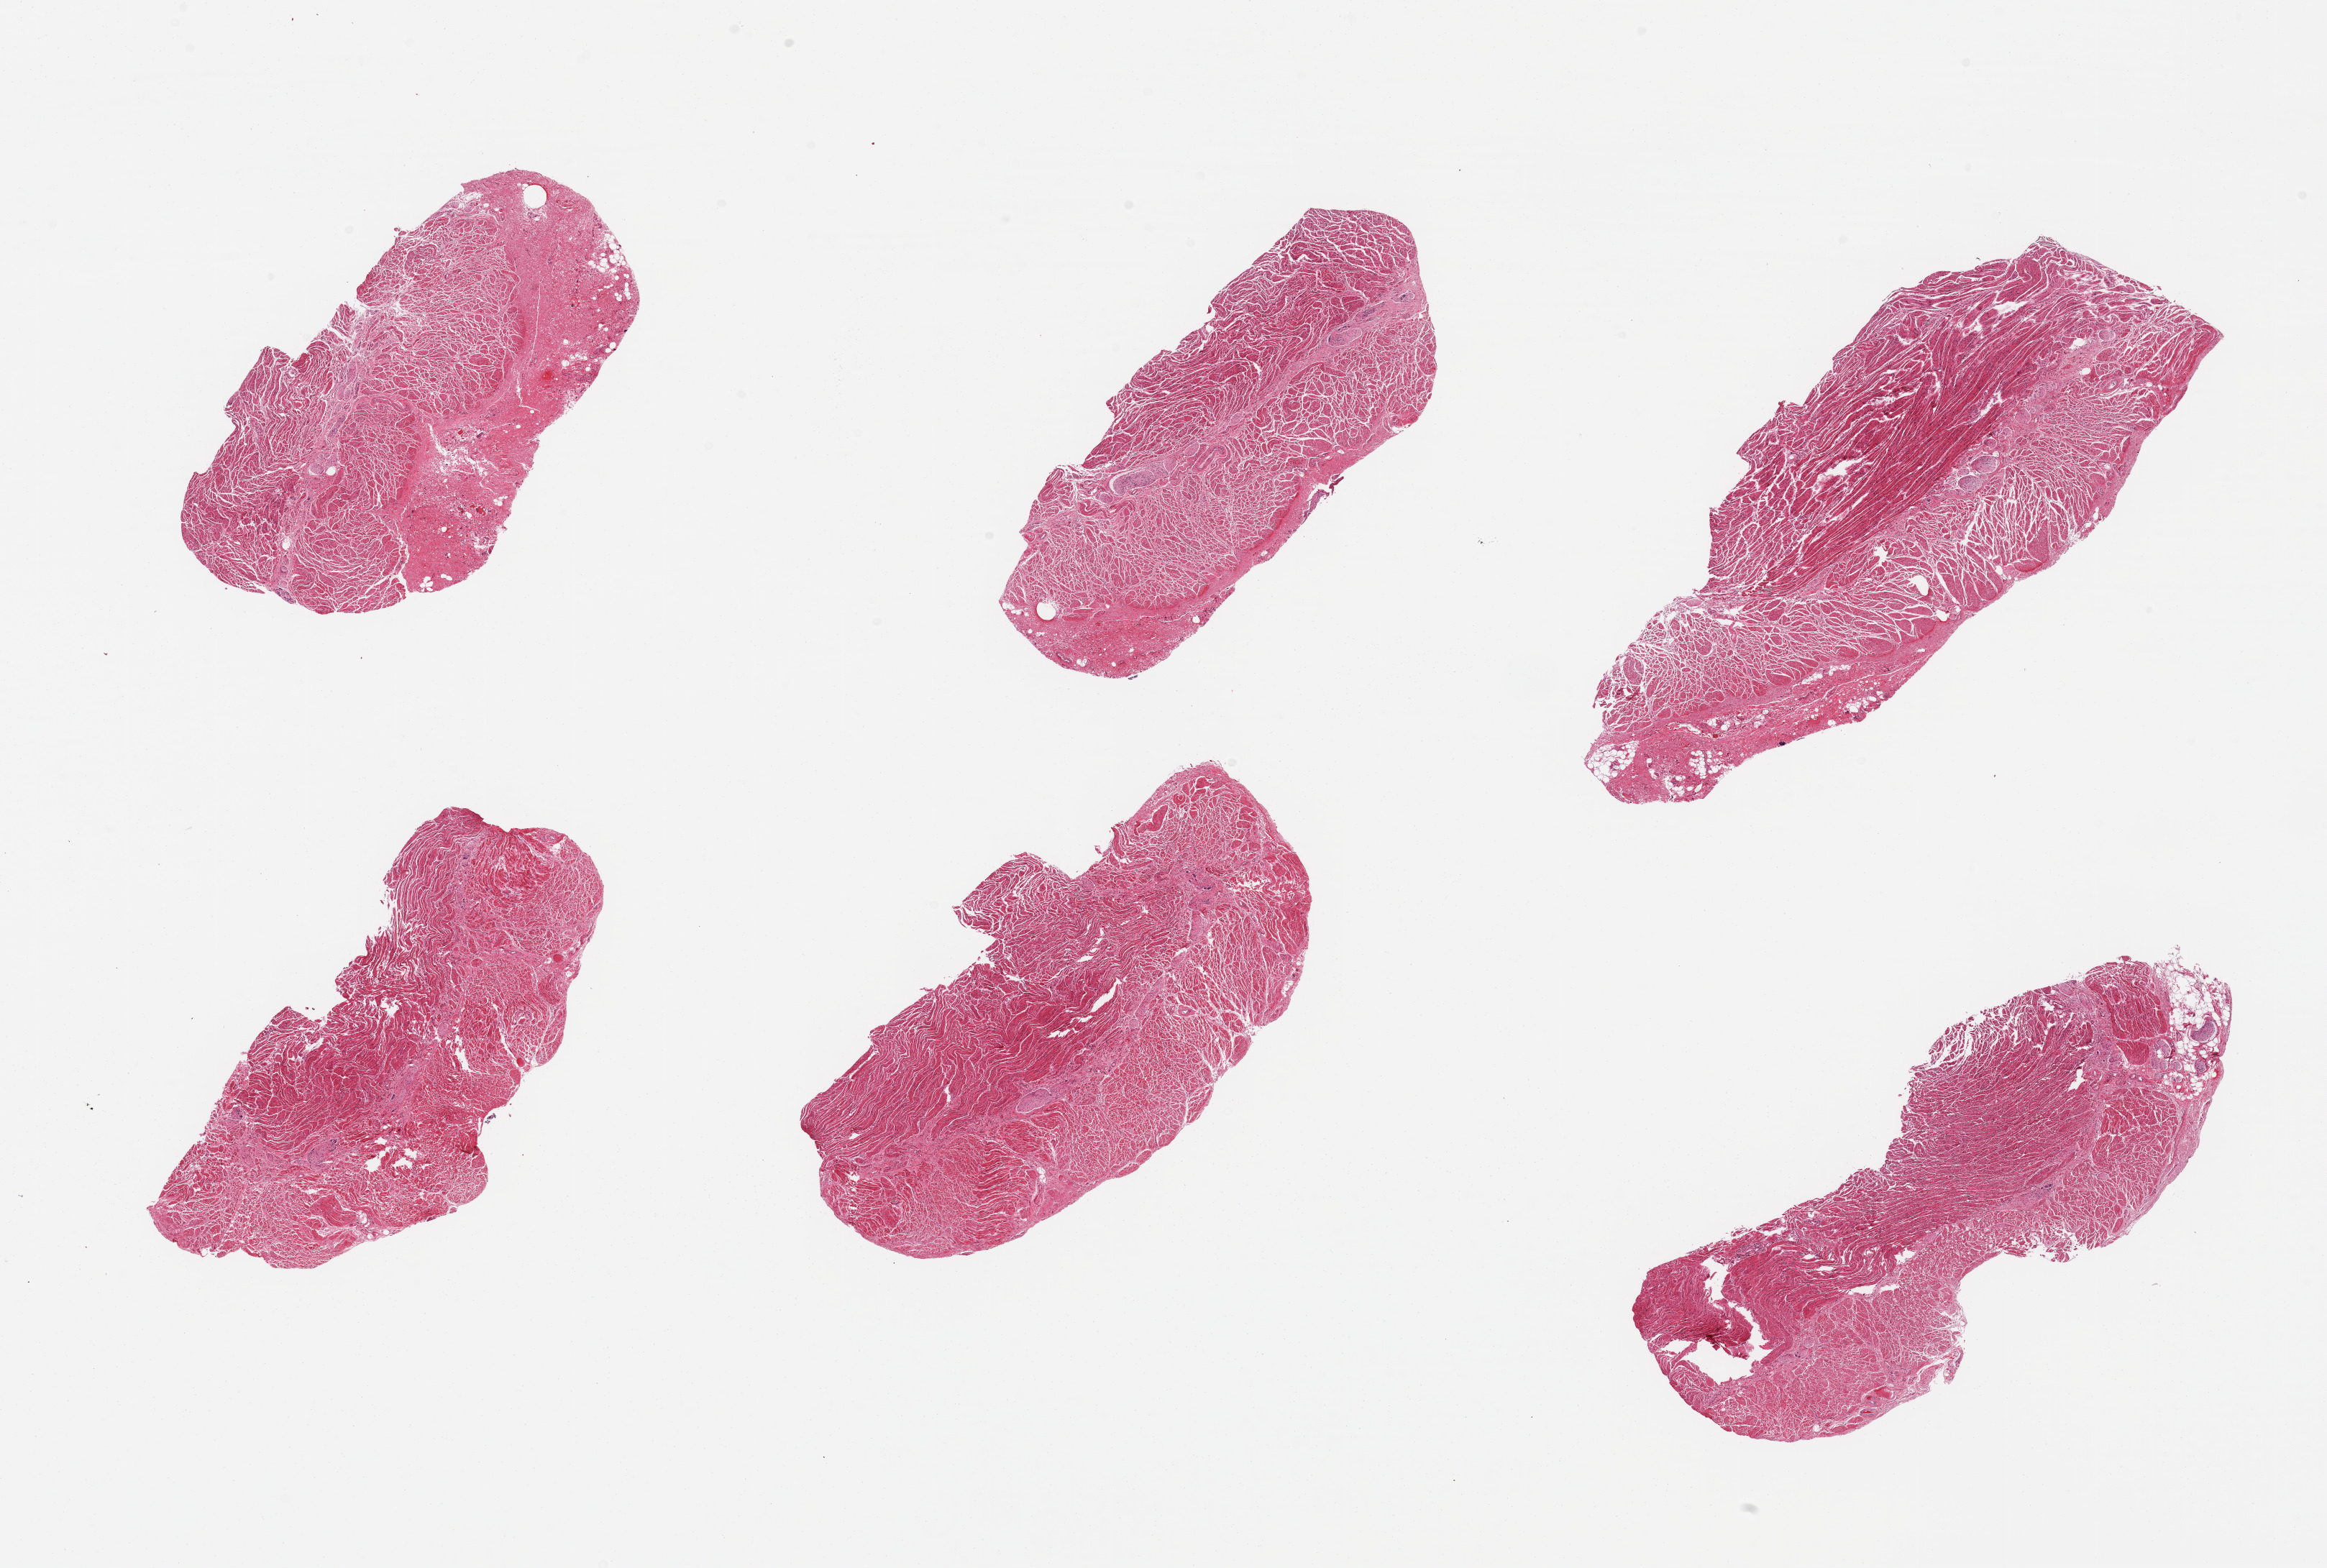
H&E whole-slide image, brightfield — a low-resolution overview of the entire scanned area, about 25.6 x 17.3 mm (acquisition: 20x scan). PAXgene-fixed, paraffin-embedded tissue. Sampled site (target tissue): gastroesophageal junction. Tissue donor sample. Donor: male.
Review note (as recorded): 6 pieces, confirmed target muscularis.